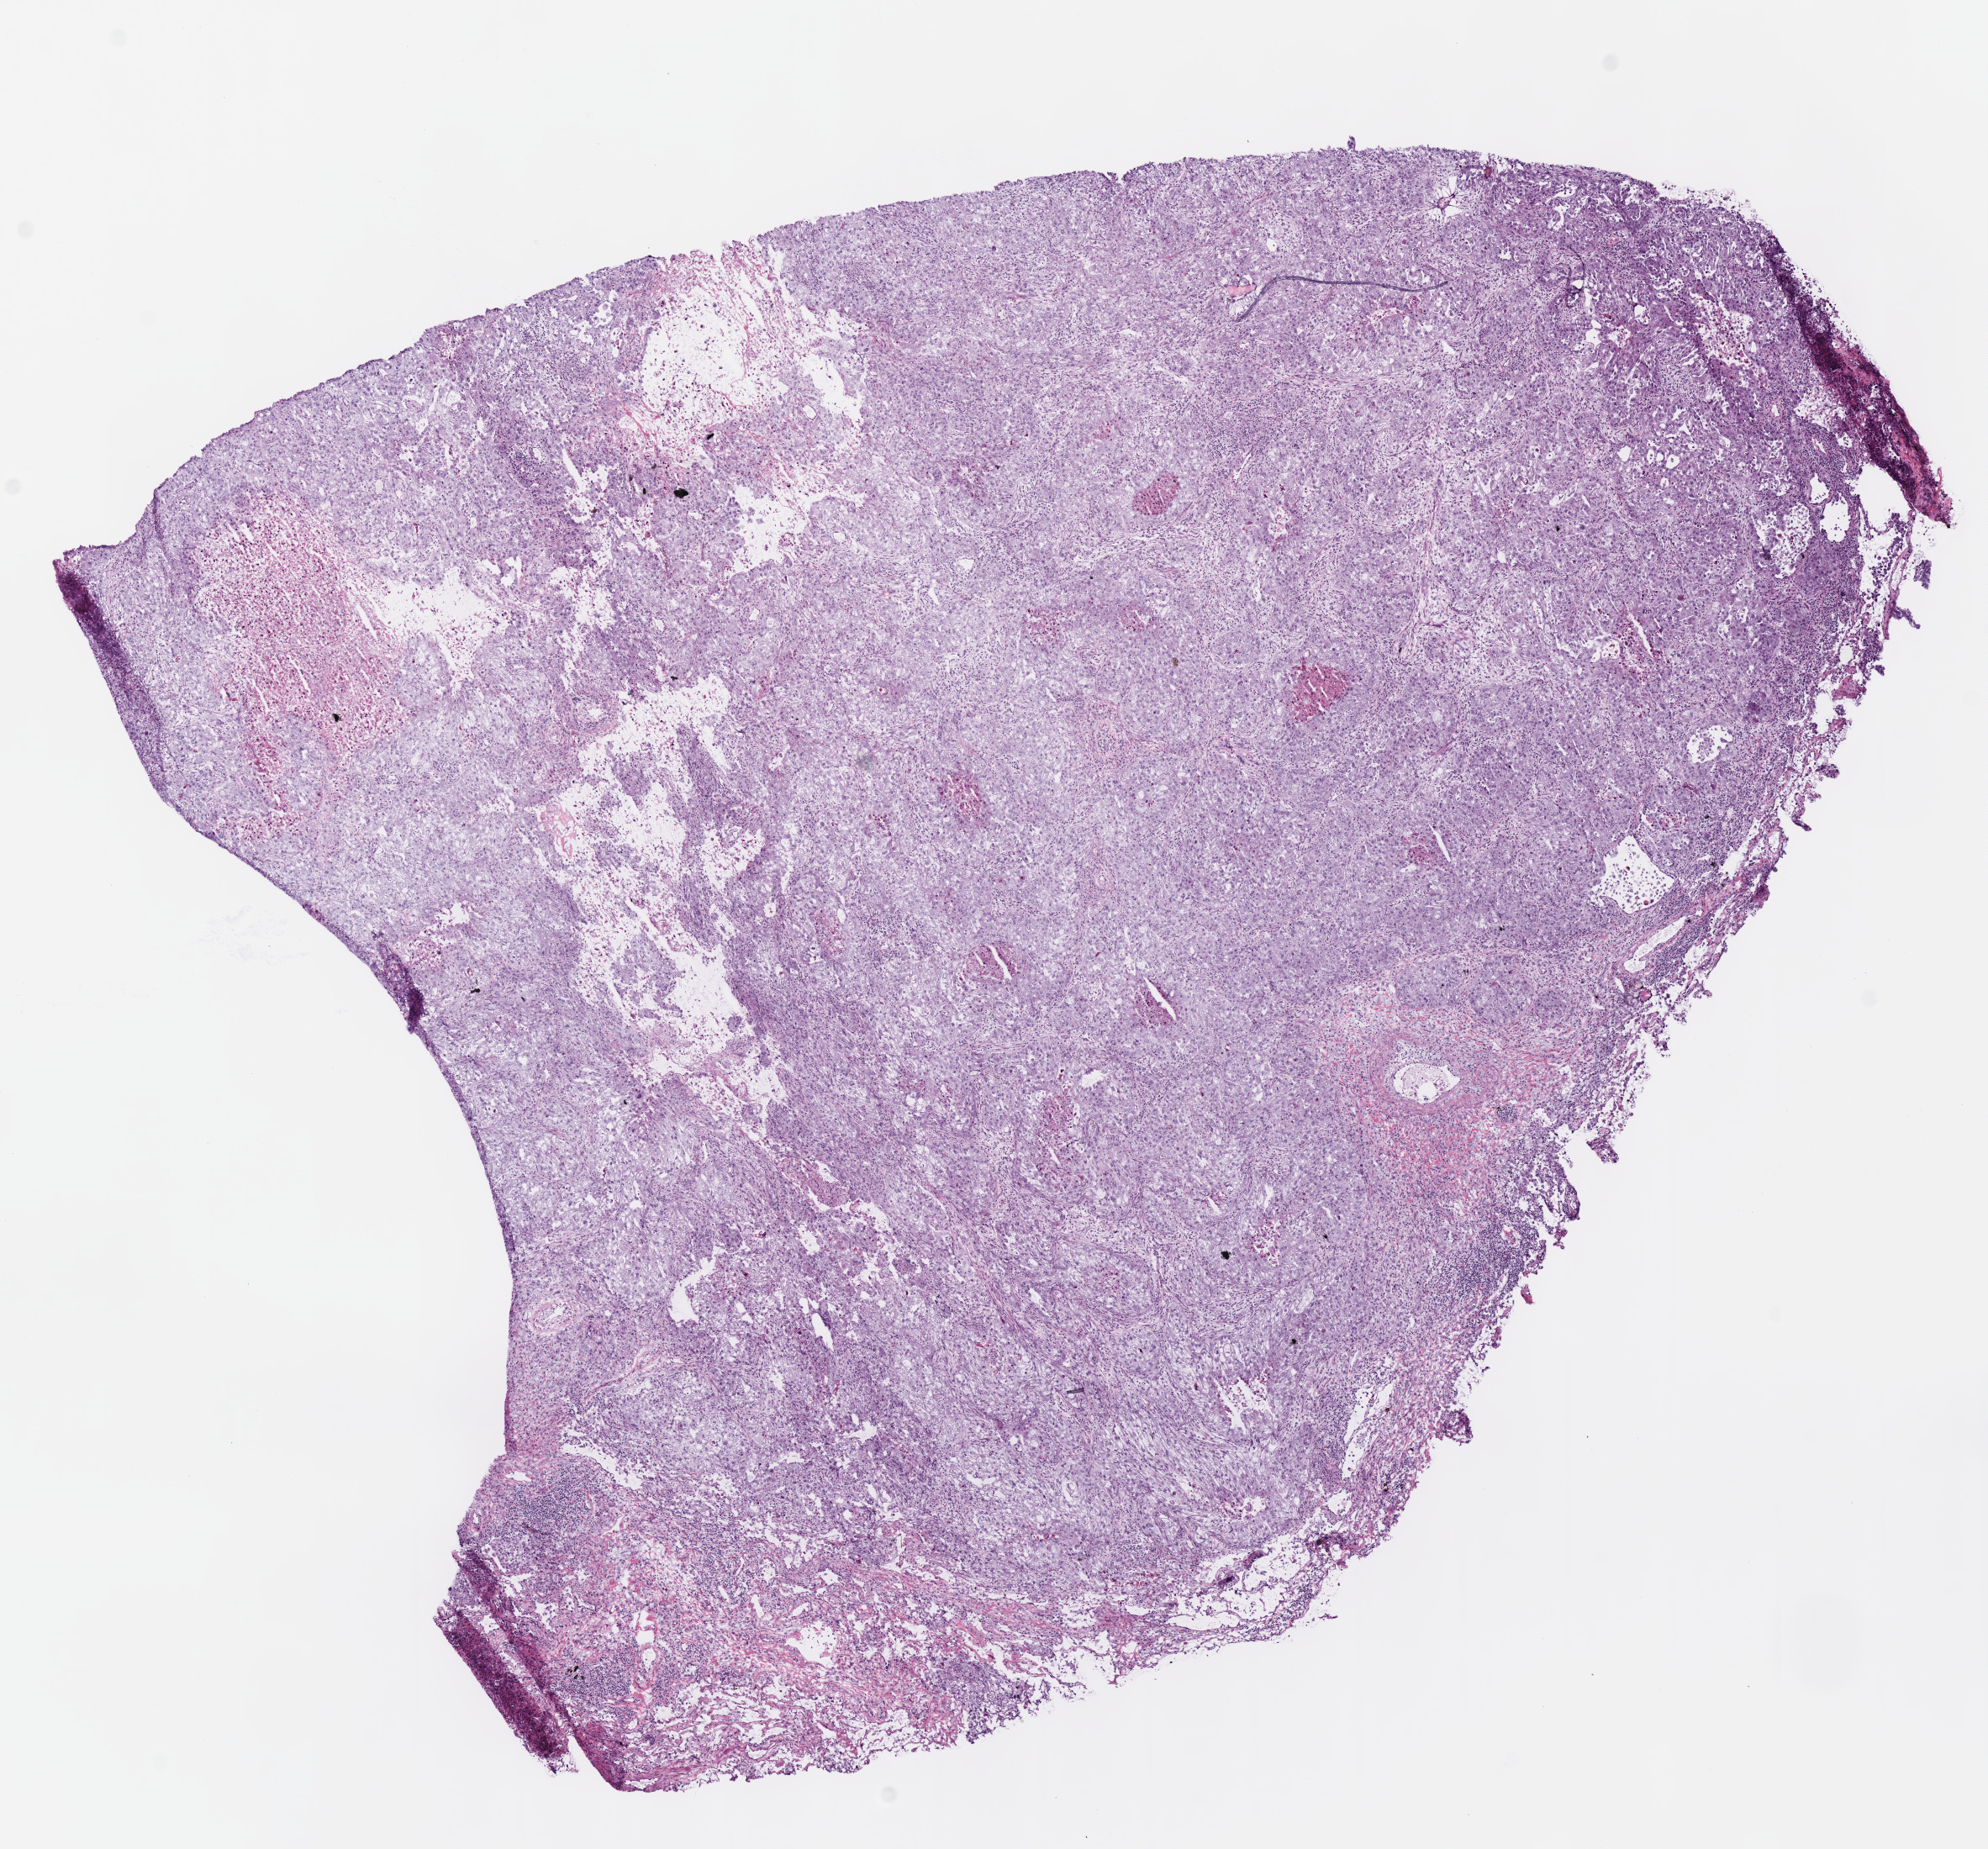
Digitized Hematoxylin and eosin (H&E) stained tissue section (whole slide) — whole scanned area (about 9.3 x 8.7 mm) shown as a low-resolution overview. Frozen section. Primary tumour sample from the lung. Female patient; age at initial diagnosis 69 years. Slide review estimates, as recorded: tumour cells 82%, tumour nuclei 75%, normal cells 5%, stromal cells 5%, necrosis 8%.
Laterality: right. AJCC pathologic stage: IB. TNM: T2a N0 M0. Diagnosis: Adenocarcinoma, NOS.